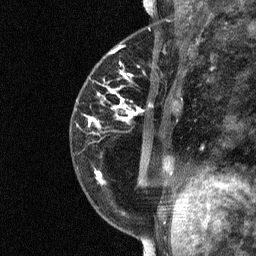
Breast MRI (dynamic contrast-enhanced), one sagittal slice; slice 22 of 64 in the series (ordered by position); dynamic contrast-enhanced study with each time point stored as its own series, time point 2 of 3 at this slice position (early post-contrast, ordered by acquisition time); 1.5 T; TE 4.8 ms, TR 27 ms; 2 mm slice thickness; 256 × 256 image matrix, field of view 180 × 180 mm. Patient: female, 34 years. From the clinical record (not read from this slice): setting: breast cancer imaged before/during neoadjuvant chemotherapy; receptor status: HR-positive, HER2-negative.
Outlined on this slice (semi-automatic segmentation, software-assisted and operator-edited):
- analysis volume of interest (the breast-tissue region the enhancement analysis was run in; not a lesion): bounding box <78,44,181,191> (left, top, right, bottom; pixels)
- tumour enhancement mask (voxels above the 90 % enhancement threshold inside the analysis volume of interest): <89,73,134,182>